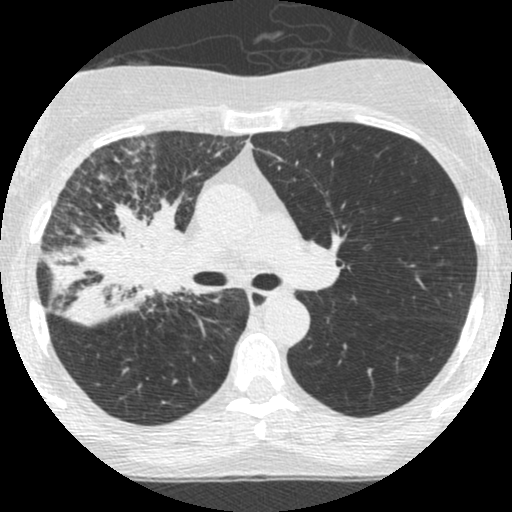
Low-dose screening chest CT, one axial slice. Position 163 of 253 along the scan axis. Reconstruction kernel STANDARD. 120 kVp. Lung window (W 1500 / L -600 HU). 512 × 512 image matrix, field of view 294 × 294 mm.
Structures marked on this image (outlined manually by an expert reader):
- lesion 2 (tumor, hilum of right lung): bounding box <44,189,187,327> (left, top, right, bottom; pixels)